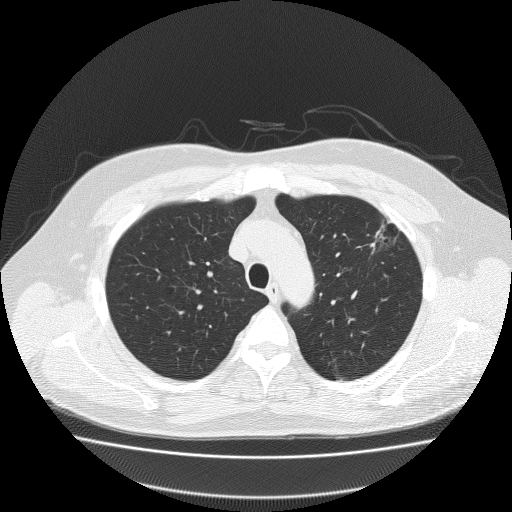
Axial slice from a low-dose chest CT screening exam. Baseline screening round. Lung window (W 1500 / L -600 HU). Lung (sharp) reconstruction kernel (FC51). Slice 48 of 204 in the series. Male, age 62 years at enrolment.
Expert-annotated lung lesion, bounding box (x1, y1, x2, y2) in pixels: (349, 213, 417, 266). Screening reader's record for this exam (one nodule recorded; not confirmed to be the boxed lesion): non-calcified nodule or mass ≥4 mm, left upper lobe, 18 × 8 mm, spiculated (stellate) margins, soft tissue attenuation. Participant outcome: lung cancer diagnosed 49 days after this screen — bronchiolo-alveolar adenocarcinoma, NOS, left upper lobe, well differentiated (G1), stage IA (AJCC 6th edition), 25 mm at pathology.